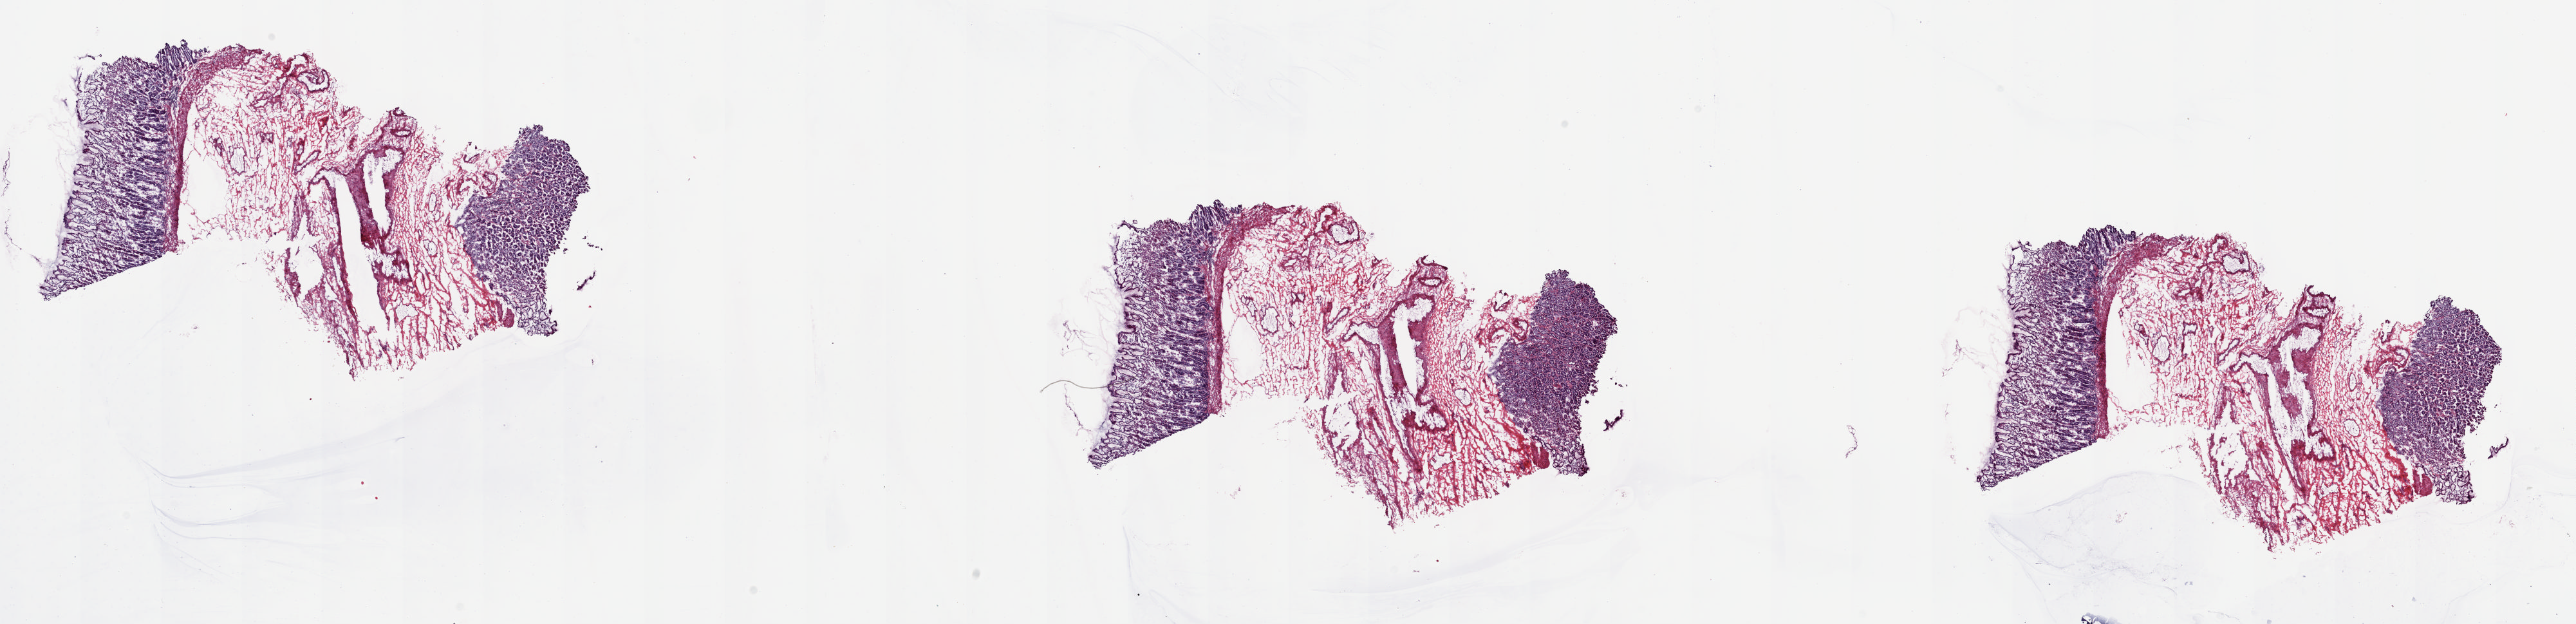
H&E-stained whole-slide image — shown as a low-resolution overview of the whole scanned area (about 31.7 x 7.7 mm, slide scanned at 20x); frozen section from the top of the tissue portion; sample: solid tissue normal (non-tumour tissue), esophagus. Patient: male, age at initial diagnosis 75 years. Slide review estimates, as recorded: tumour cells 0%, tumour nuclei 0%, normal cells 100%, stromal cells 0%, necrosis 0%. Infiltration values recorded for this section: lymphocyte infiltration 2%, monocyte infiltration 0%, neutrophil infiltration 0%.
This section: solid tissue normal (non-tumour) sample from the same patient. Patient diagnosis: Adenocarcinoma, NOS (lower third of esophagus).